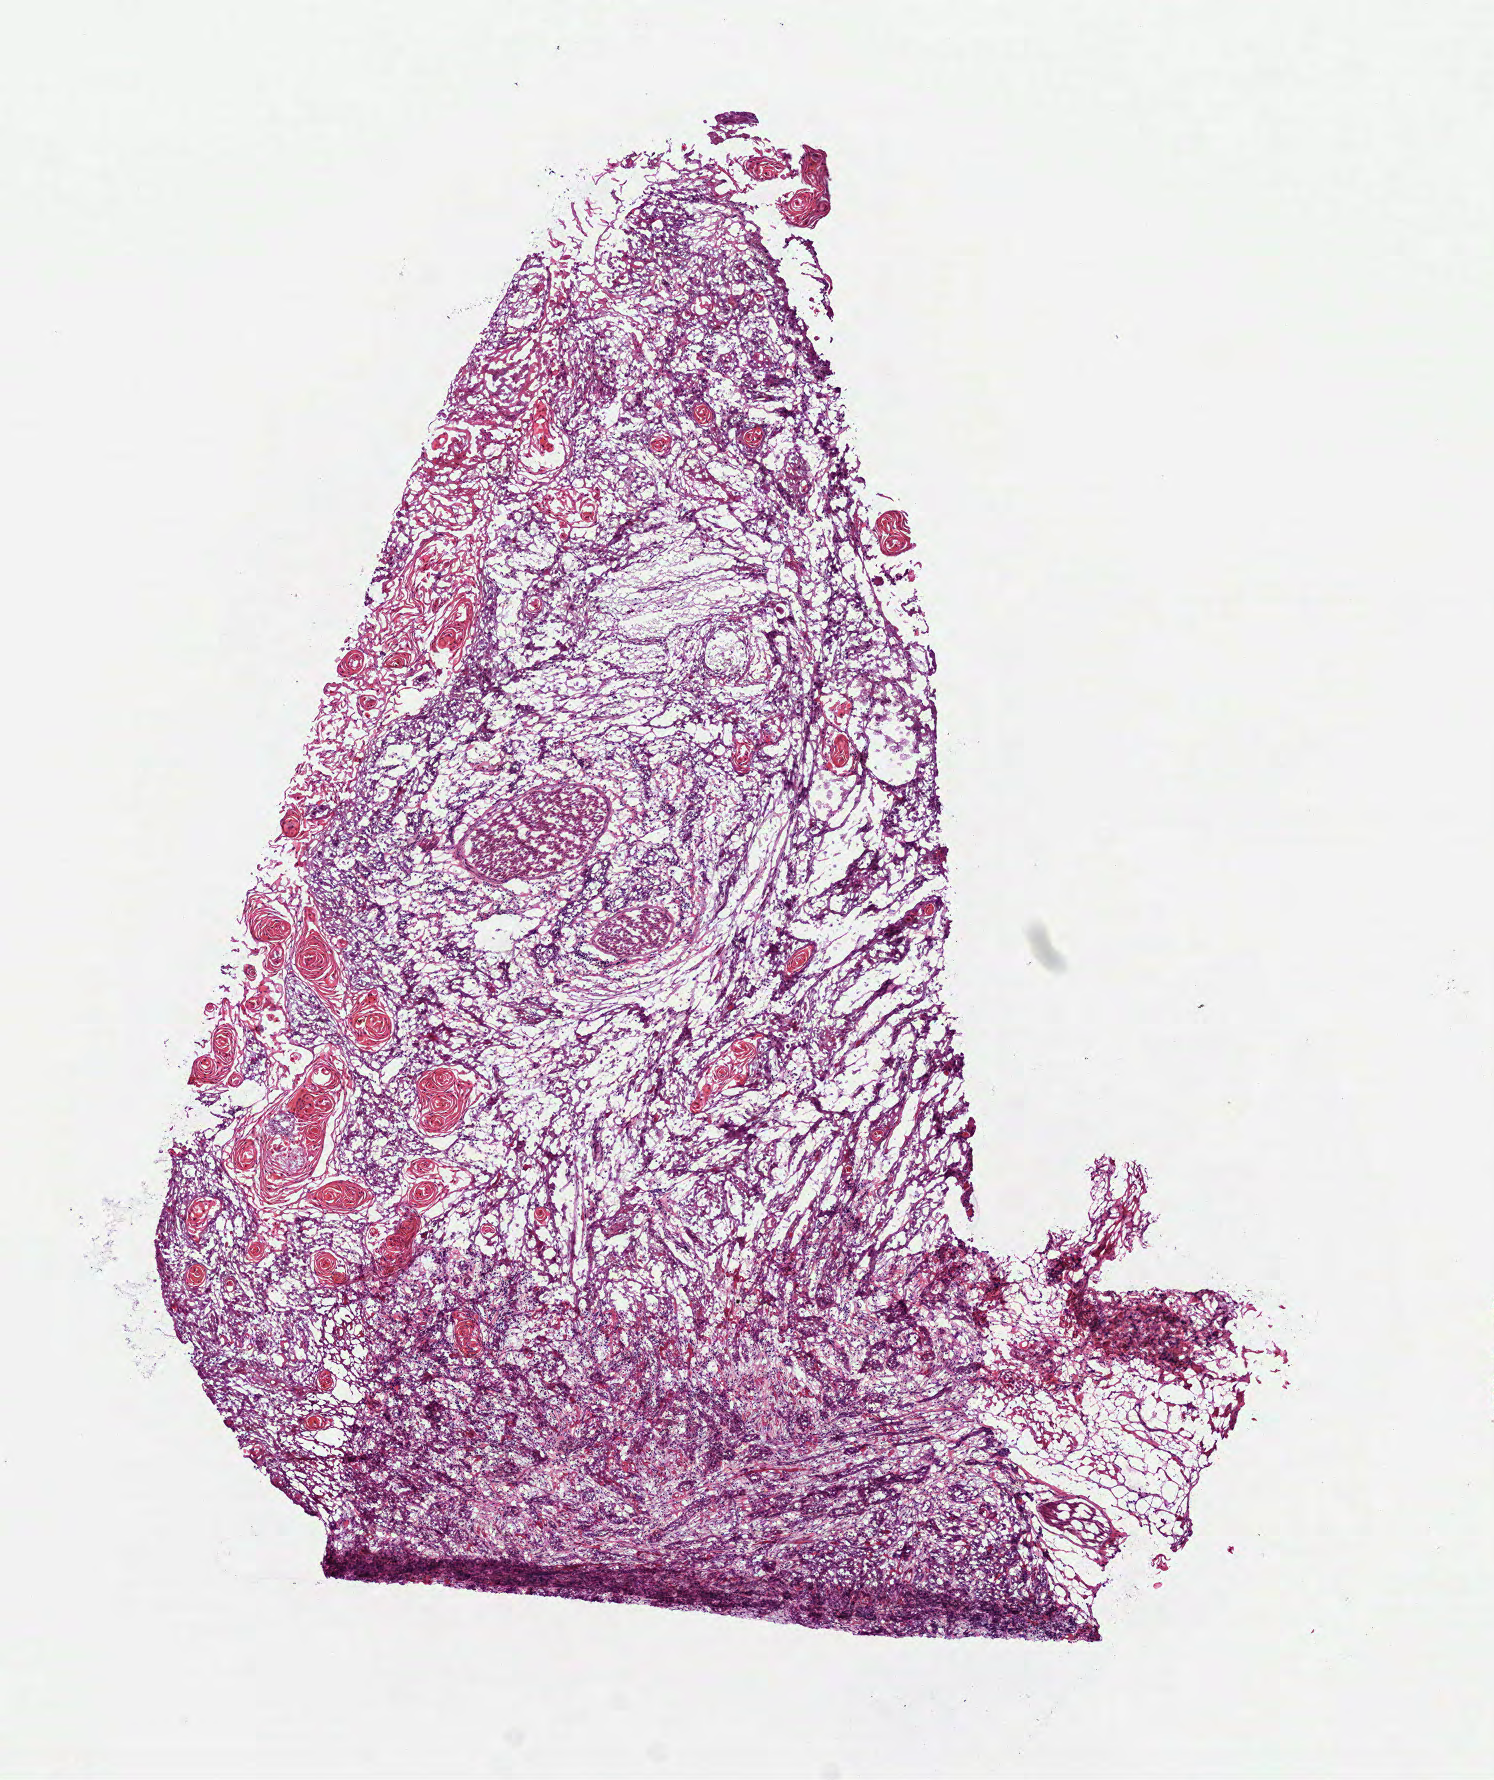
Whole-slide histology image, Hematoxylin and eosin (H&E) stained, shown as a low-resolution overview of the whole scanned area (about 6.0 x 7.2 mm, slide scanned at 40x); frozen section from the top of the tissue portion; primary tumour sample from the head and neck. Patient: male, age at initial diagnosis 77 years.
Histologic diagnosis: Squamous cell carcinoma, NOS (overlapping lesion of lip, oral cavity and pharynx).